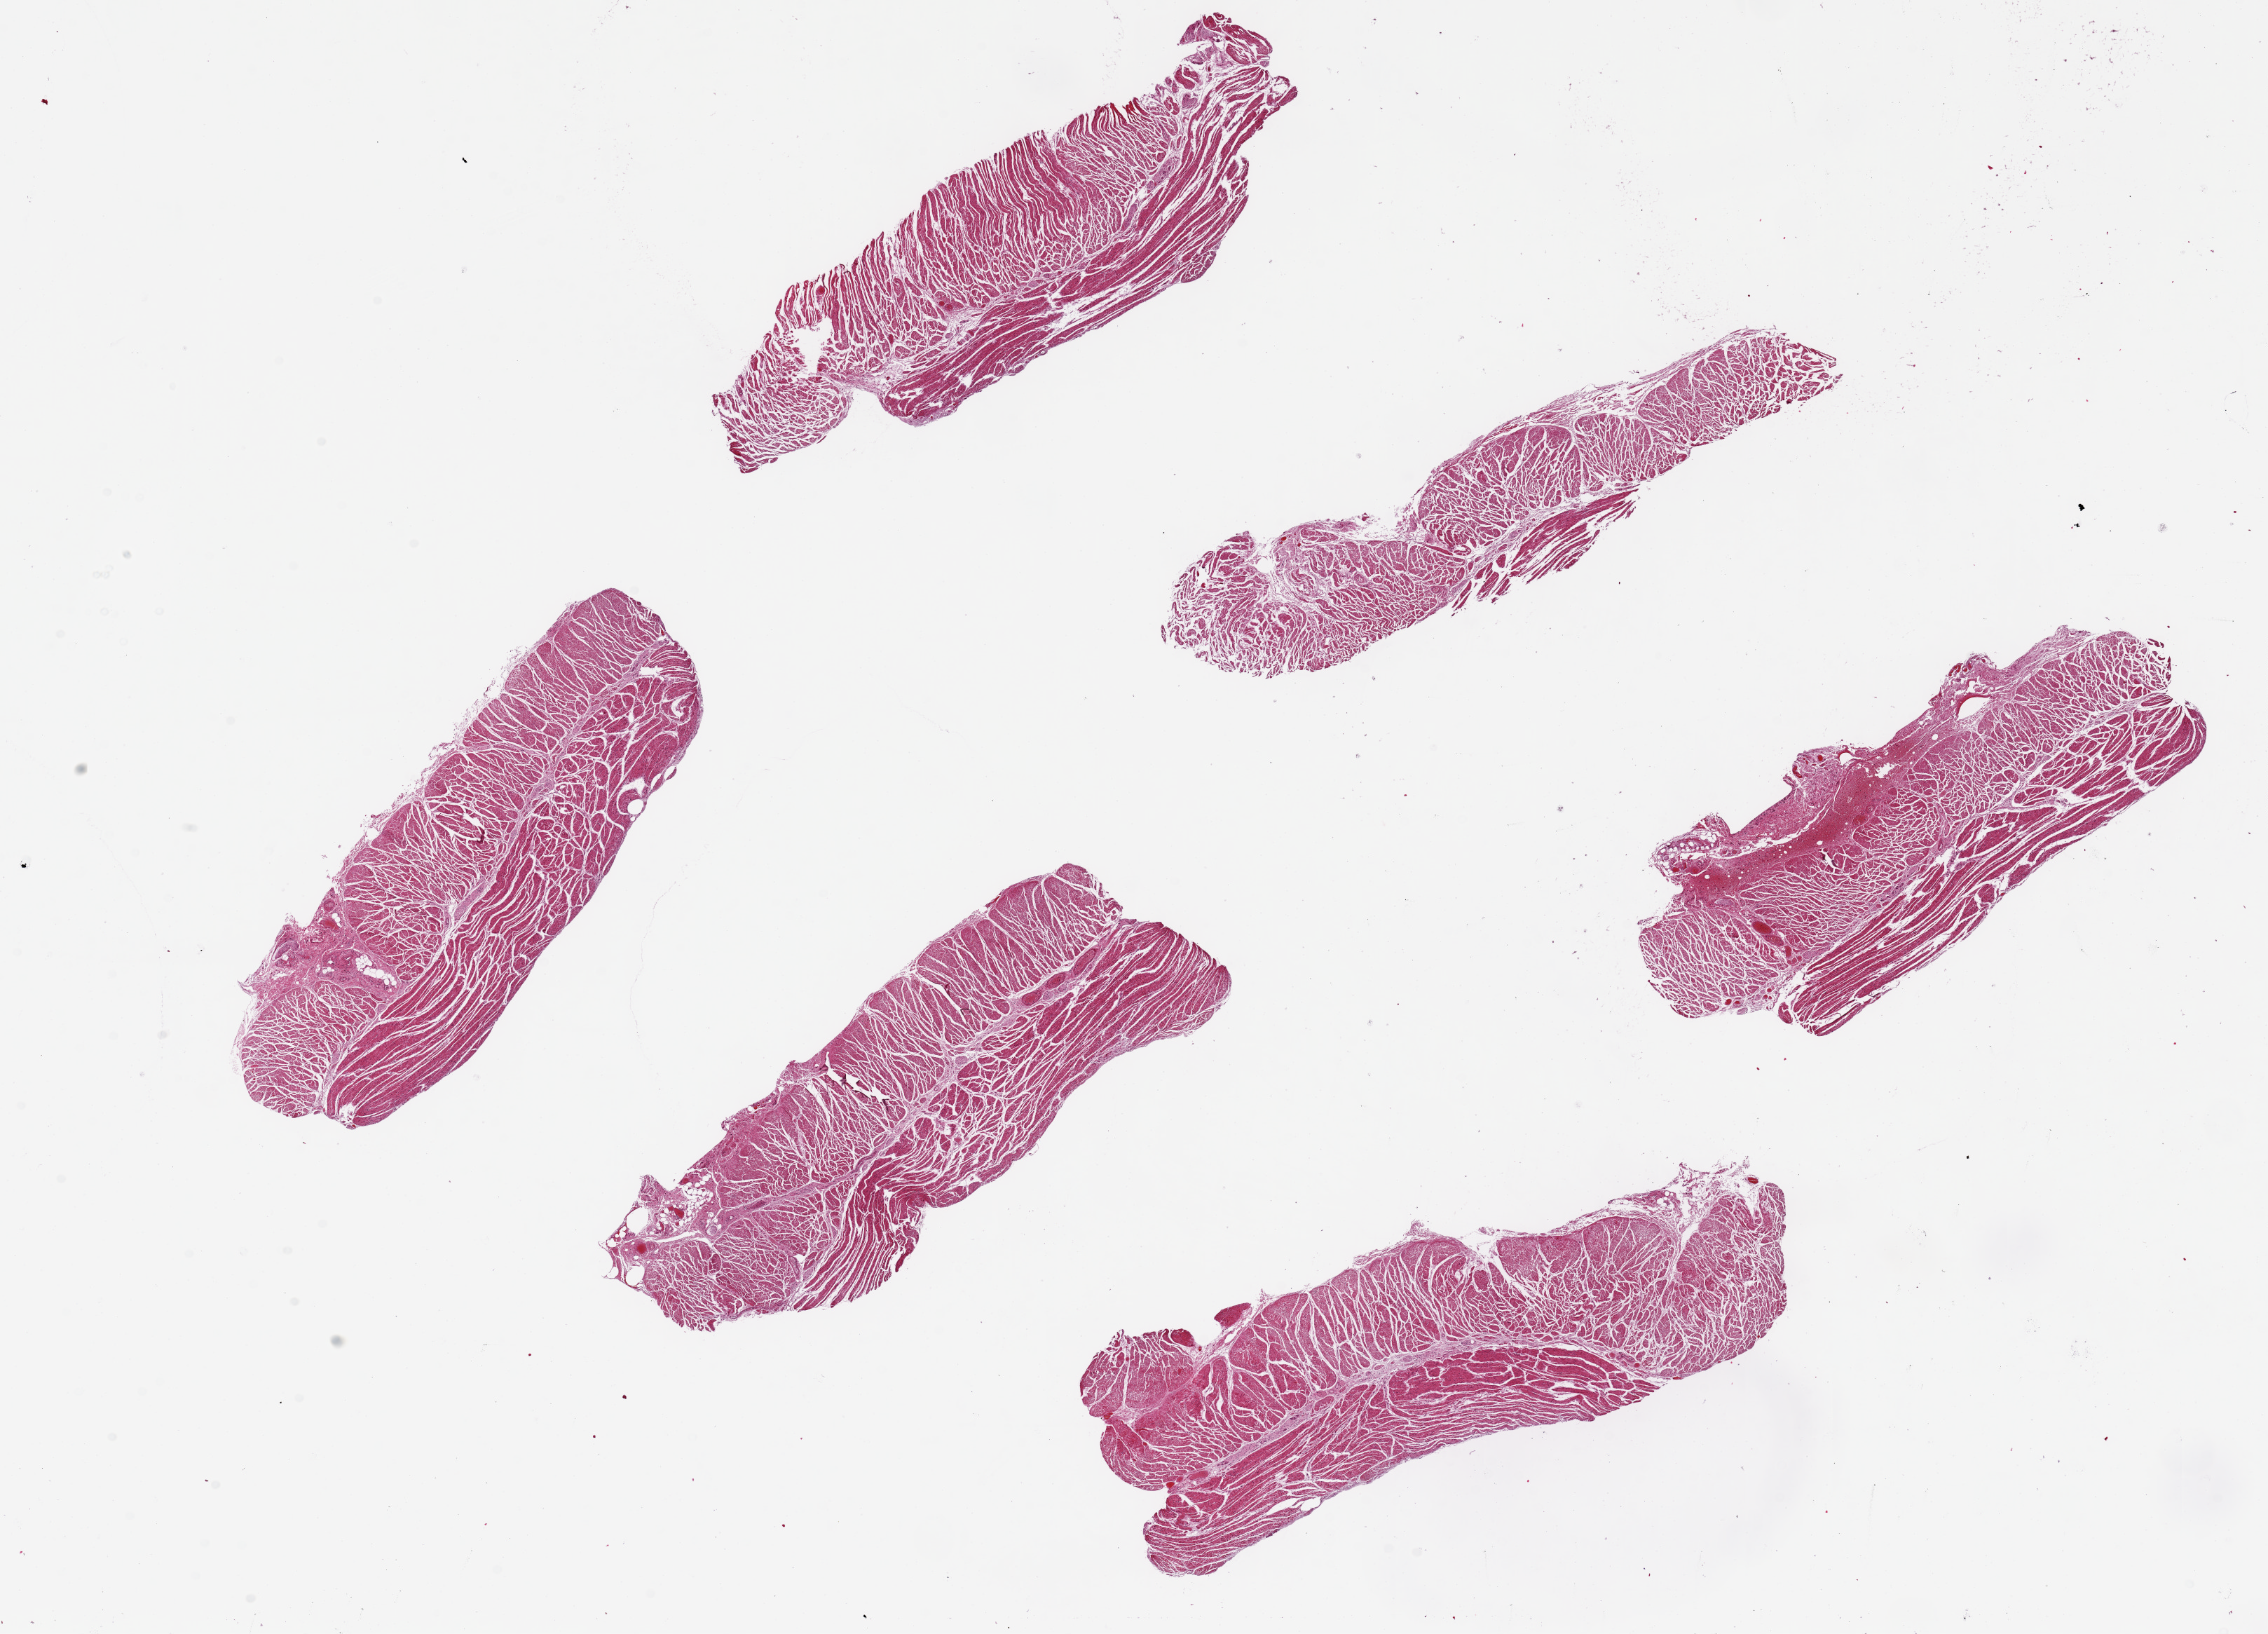
Whole-slide image, hematoxylin and eosin (H&E) stain — low-resolution overview of the scanned area, about 25.6 x 18.4 mm; PAXgene-fixed, paraffin-embedded tissue; target tissue: esophageal muscle; tissue donor sample. Donor sex: female.
Pathologist's review note for this sample: 6 pieces, up to 8x2mm all msucle.